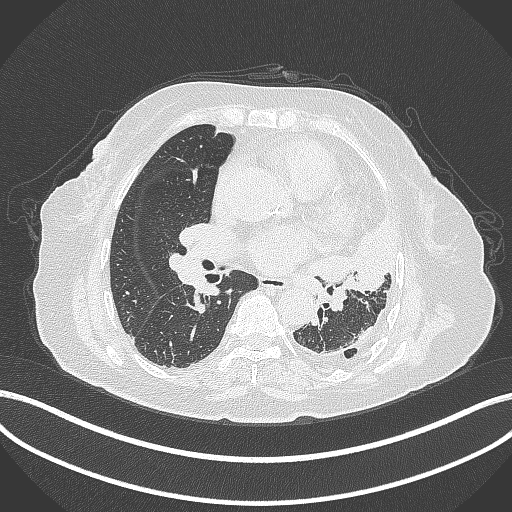
Chest CT, one axial slice. Position 186 of 399 along the scan axis. 120 kVp. Lung window (W 1500 / L -600 HU). 1 mm slice thickness. 512 × 512 image matrix. Patient: female, 75 years. Case-level facts recorded for this patient, not image findings: clinical TNM (as recorded): T3 N3 M1.
Annotated regions visible in this slice (bounding box drawn by a radiologist):
- lung tumour (recorded histology: adenocarcinoma): bounding box (x1, y1, x2, y2) in pixels: (306, 217, 399, 294)